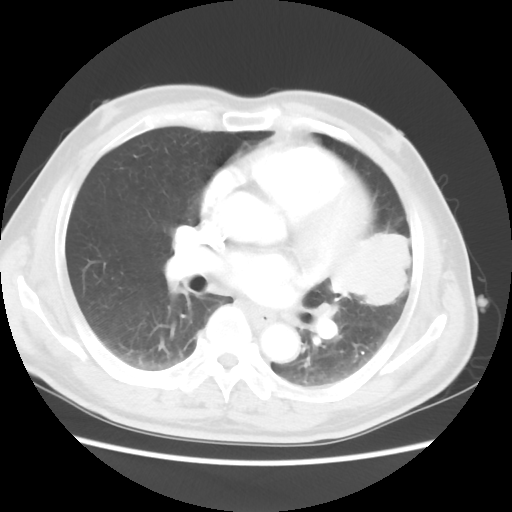
Chest CT, one axial slice; slice 25 of 50 in the series (ordered by position); reconstruction kernel STANDARD; lung window (W 1500 / L -600 HU); 5 mm slice thickness; 512 × 512 image matrix, field of view 360 × 360 mm. Male patient, age 69 years. From the clinical record (not read from this slice): clinical TNM (as recorded): T3 N1 M1a.
Annotated regions visible in this slice (bounding box drawn by a radiologist):
- lung tumour (recorded histology: squamous cell carcinoma): bounding box [x1, y1, x2, y2] px = [317, 207, 419, 324]